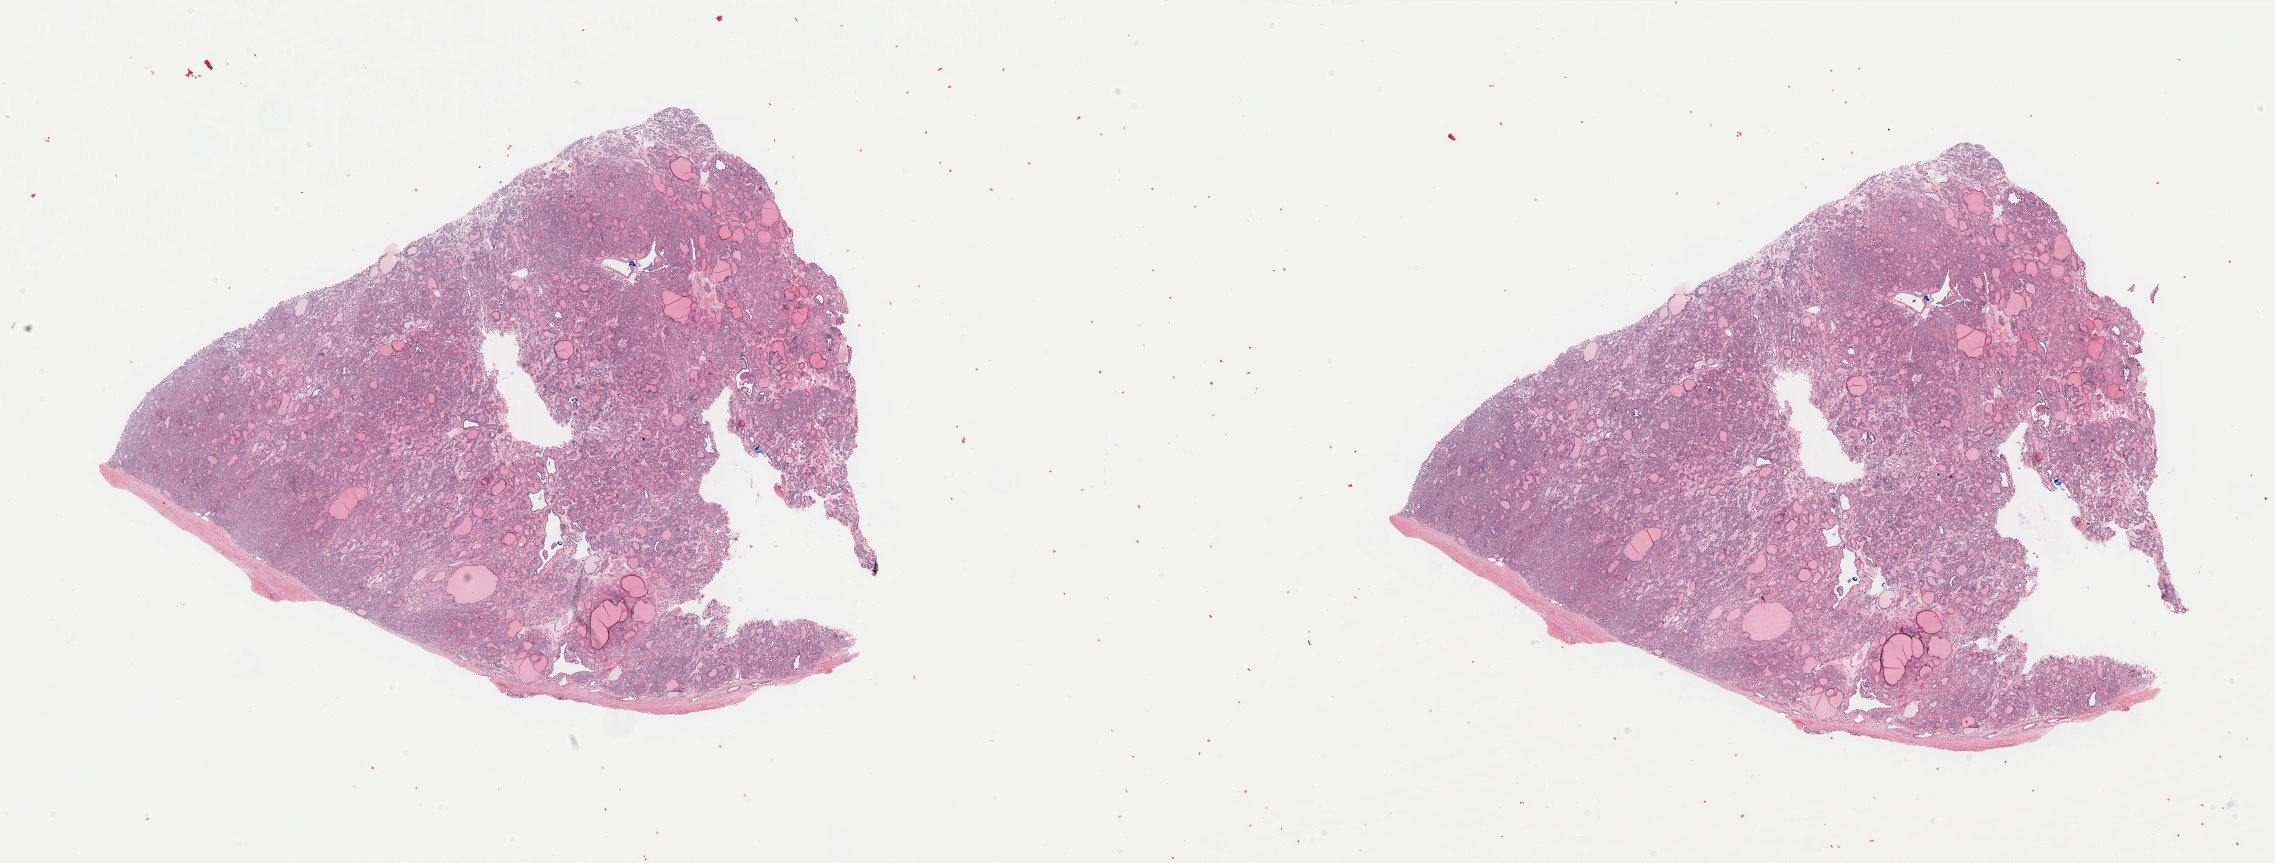
Whole-slide histology image, H&E-stained — shown as a low-resolution overview of the whole scanned area (about 36.0 x 13.7 mm, slide scanned at 40x); formalin-fixed paraffin-embedded (FFPE) diagnostic section; primary tumour sample from the thyroid. Patient: female, age at initial diagnosis 44 years.
• laterality: right
• histologic diagnosis: Papillary carcinoma, follicular variant (thyroid gland)
• TNM: T2 NX MX
• AJCC pathologic stage: I